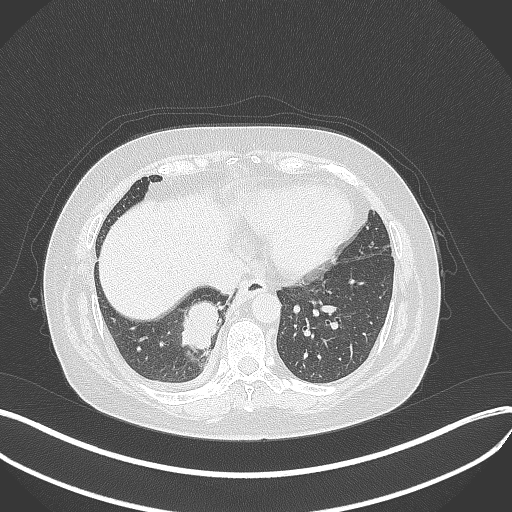
Chest CT, one axial slice. Slice 105 of 381 in the series (ordered by position). 120 kVp. Lung window (W 1500 / L -600 HU). 1 mm slice thickness. 512 × 512 image matrix. Patient: female, 56 years. Case-level facts recorded for this patient, not image findings: clinical TNM (as recorded): T2b N1 M0; histopathological grade: G3.
Annotated regions visible in this slice (bounding box drawn by a radiologist):
- lung tumour (recorded histology: small cell carcinoma): box from (x=184, y=298) to (x=221, y=353) px